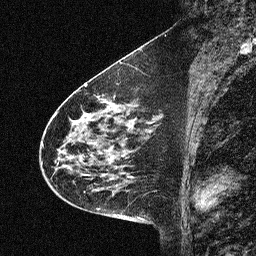
Breast MRI (dynamic contrast-enhanced), one sagittal slice; position 24 of 64 along the scan axis; dynamic contrast-enhanced study with each time point stored as its own series, time point 2 of 3 at this slice position (early post-contrast, ordered by acquisition time); 1.5 T; TE 4.5 ms, TR 11 ms; 2.06 mm slice thickness; 256 × 256 image matrix, field of view 200 × 200 mm. Patient: female, 46 years. Case-level facts recorded for this patient, not image findings: setting: breast cancer imaged before/during neoadjuvant chemotherapy; receptor status: HER2-positive.
Structures marked on this image (semi-automatic segmentation, software-assisted and operator-edited):
- analysis volume of interest (the breast-tissue region the enhancement analysis was run in; not a lesion): box from (x=42, y=80) to (x=150, y=180) px
- tumour enhancement mask (voxels above the 90 % enhancement threshold inside the analysis volume of interest): (x=55, y=100)–(x=116, y=178)